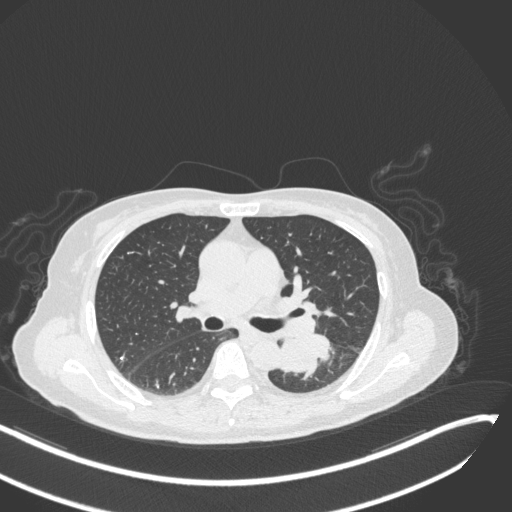
Chest CT, one axial slice; reconstruction kernel B31f; 120 kVp; lung window (W 1500 / L -600 HU); 1 mm slice thickness; 512 × 512 image matrix. Patient: female, 64 years. Case-level facts recorded for this patient, not image findings: clinical TNM (as recorded): T3 N1 M1; histopathological grade: G3.
Structures marked on this image (rectangle marked by the reading radiologist):
- lung tumour (recorded histology: small cell carcinoma): bounding box (x1, y1, x2, y2) in pixels: (277, 330, 337, 379)